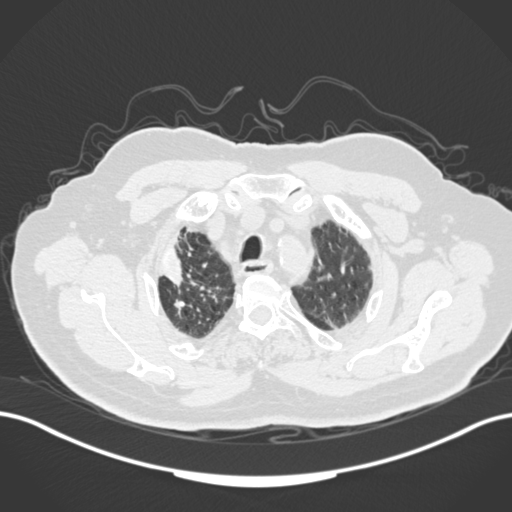
Chest CT, one axial slice; lung window (W 1500 / L -600 HU); 1 mm slice thickness; 512 × 512 image matrix, field of view 400 × 400 mm. Patient: male, 72 years. From the clinical record (not read from this slice): clinical TNM (as recorded): T1a N0 M0.
Annotated regions visible in this slice (rectangle marked by the reading radiologist):
- lung tumour (recorded histology: squamous cell carcinoma): bounding box [x1, y1, x2, y2] px = [158, 236, 190, 296]